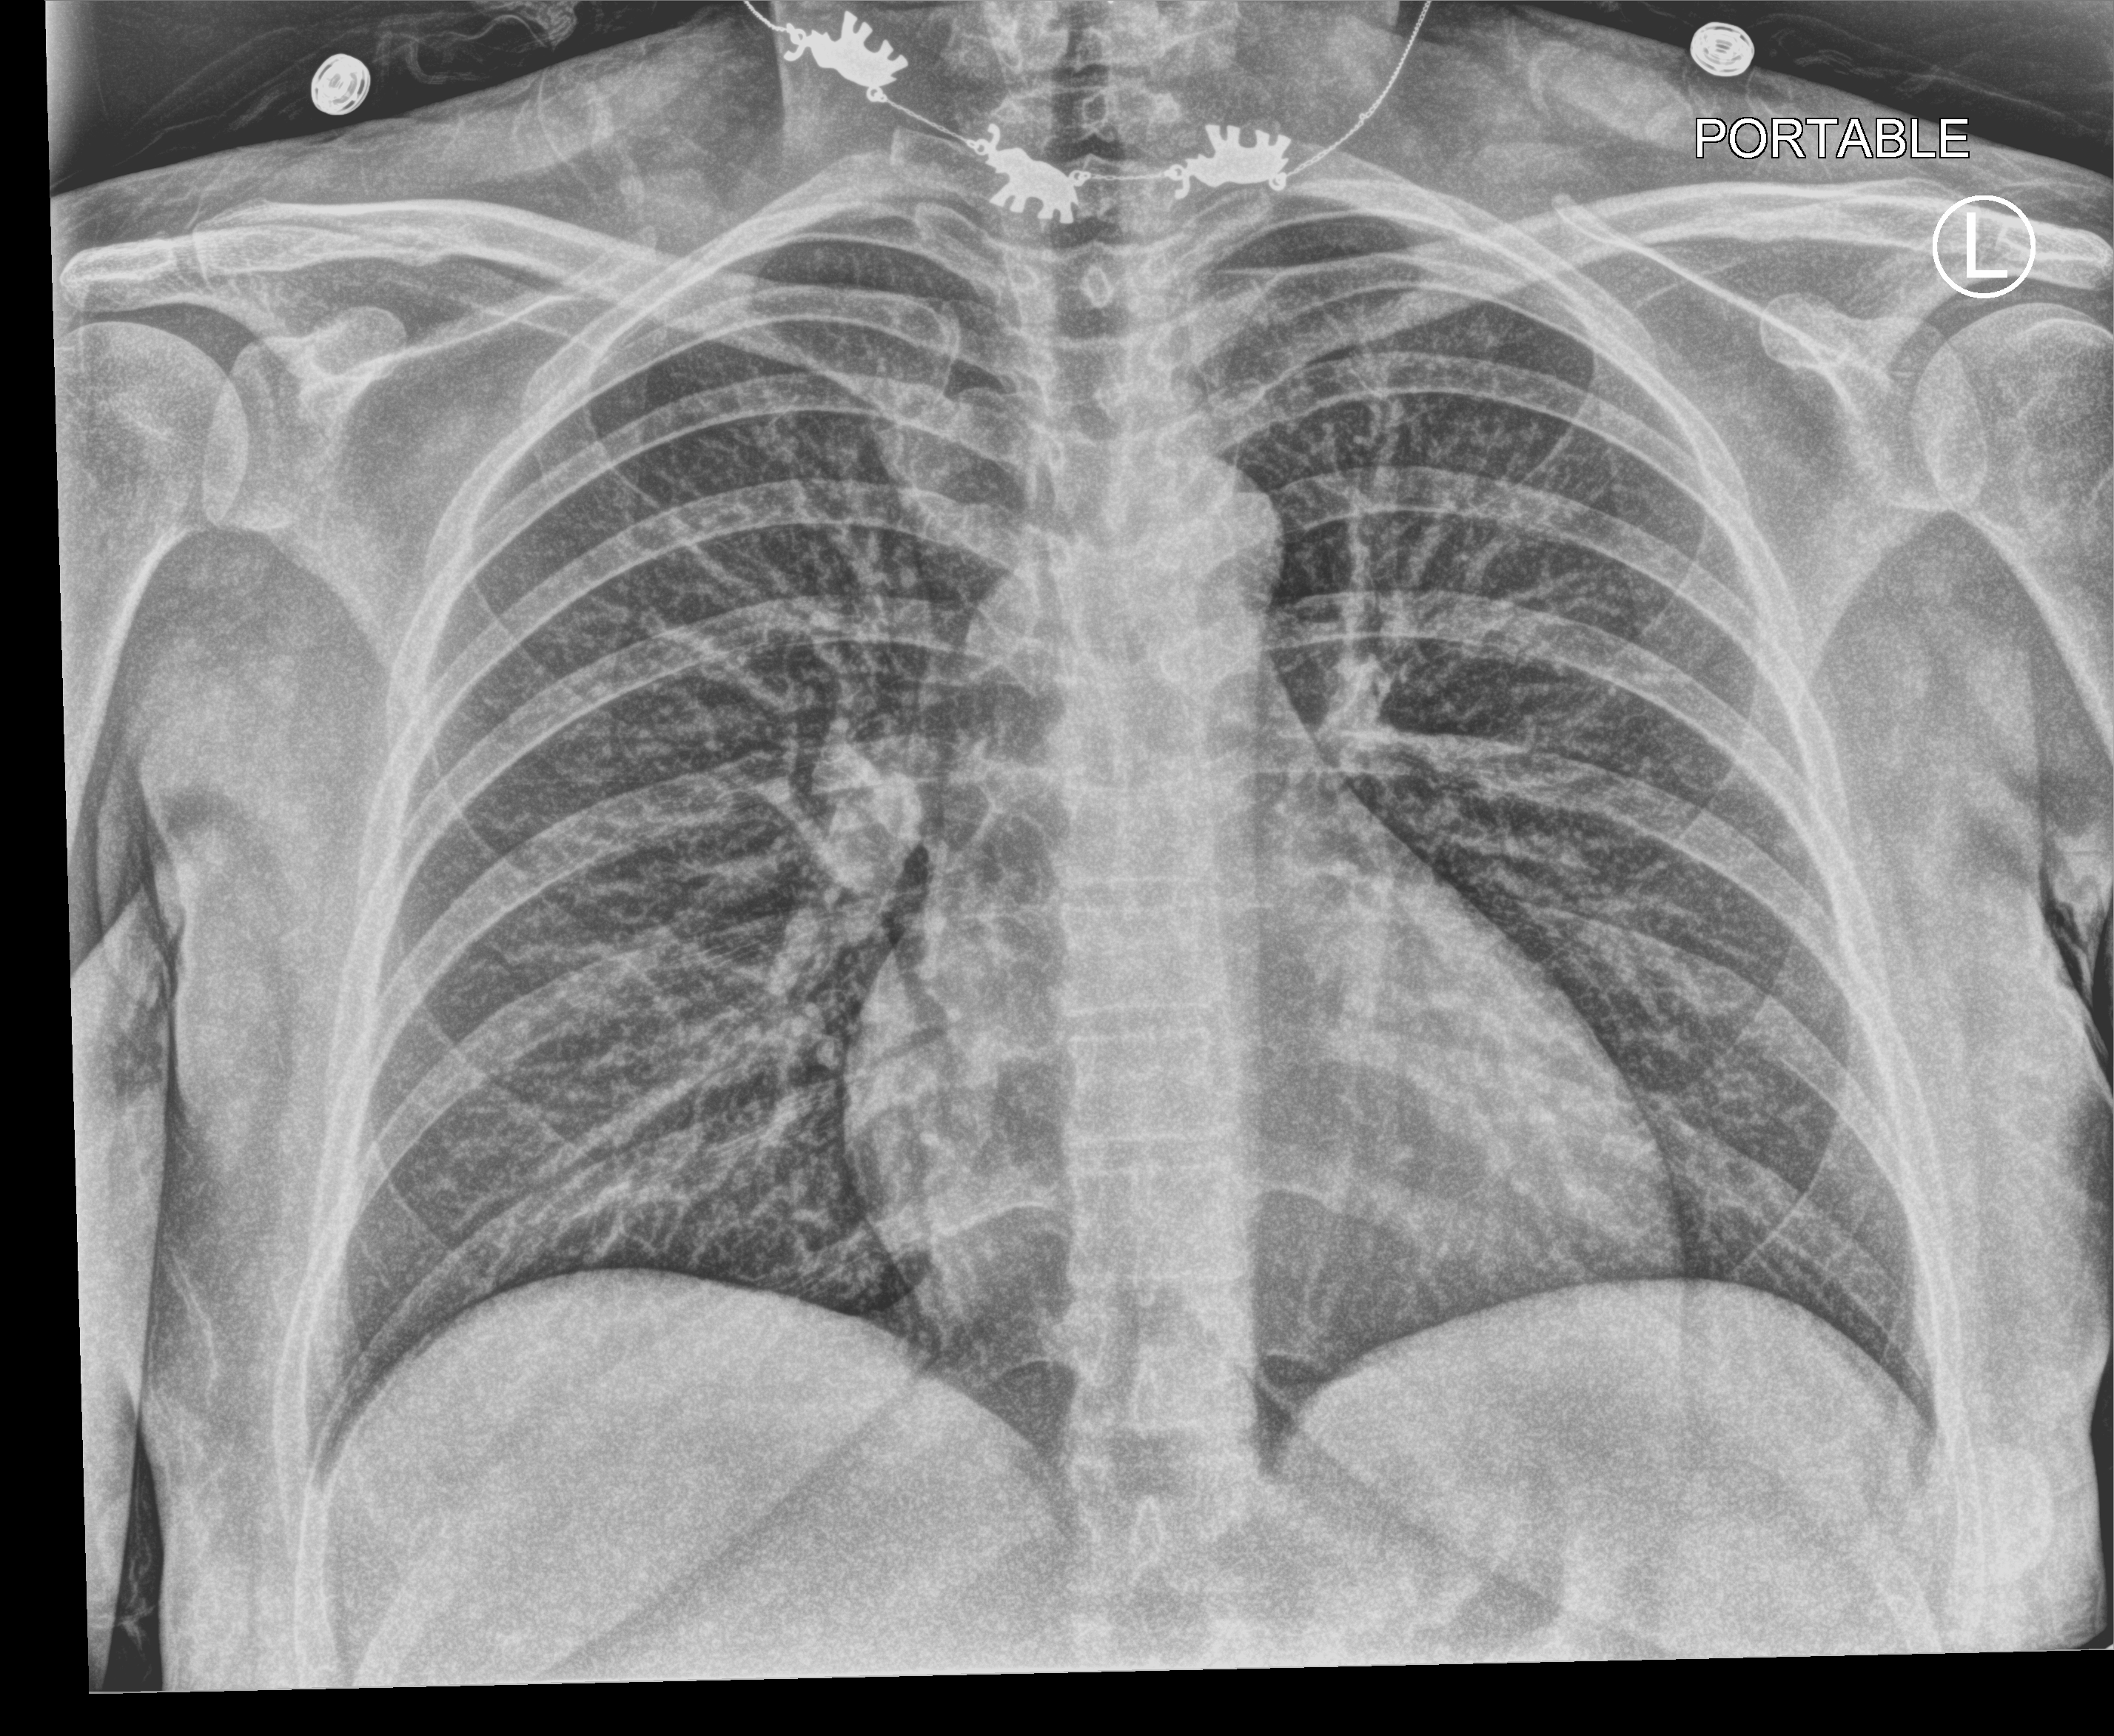
Chest X-ray (portable). Female patient hospitalised with COVID-19, age 18–59 years.
Hospital-stay facts (about this admission, not read from this image; timing relative to this image not recorded): mechanically ventilated during this hospital stay: no.